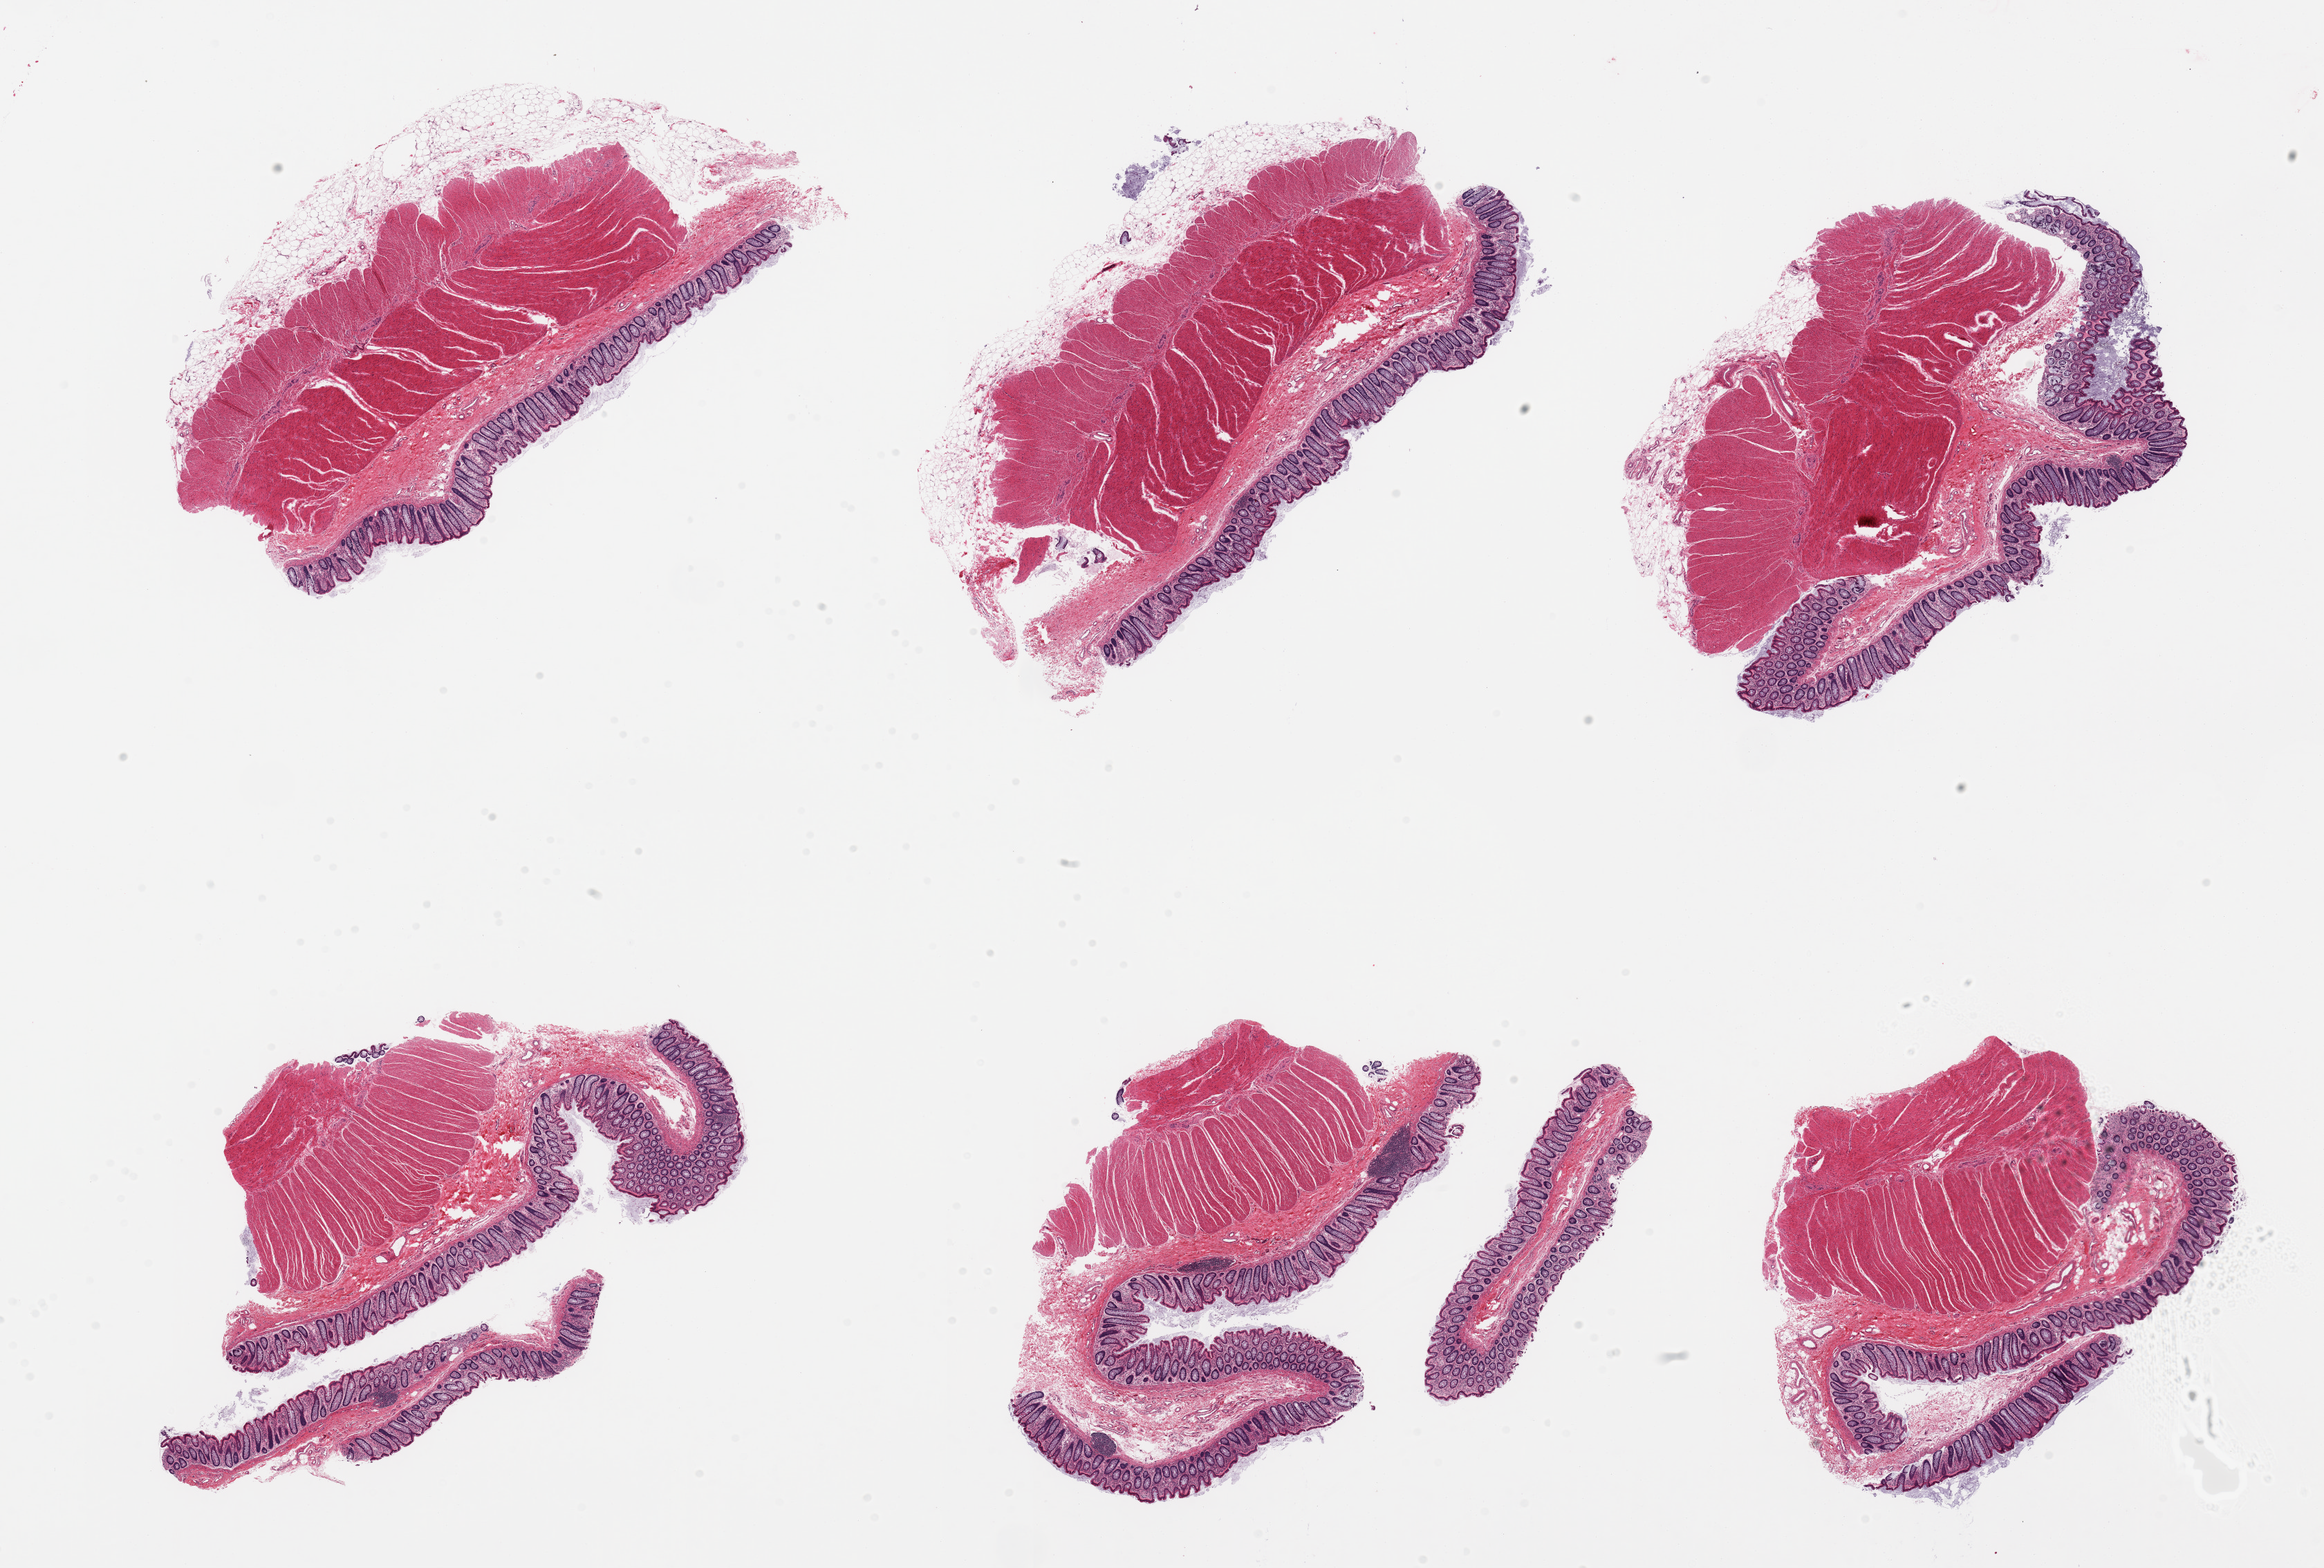
Digitized haematoxylin and eosin-stained section, brightfield, whole scanned area (about 26.6 x 17.9 mm) shown as a low-resolution overview; PAXgene-fixed paraffin-embedded (PFPE) section; section of sigmoid colon (target tissue); tissue donor sample. Donor: male.
• pathologist's review note for this sample: 7 pieces; full thickness sections with abundant mucosa (not target)